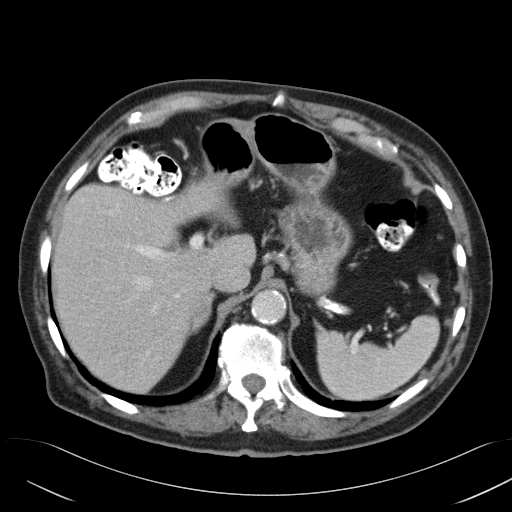
Contrast-enhanced abdominal CT, one axial slice; position 37 of 58 along the scan axis; reconstruction kernel B31f; intravenous contrast given; soft-tissue window (W 400 / L 40 HU); 5 mm slice thickness; 512 × 512 image matrix. Patient: male, 82 years. From the clinical record (not read from this slice): diagnosis: adrenocortical carcinoma; tumour side: right adrenal; tumour size at pathology: 9 cm; Ki-67 index: 30 %; stage (as recorded): 3.
Annotated regions visible in this slice (semi-automatic segmentation, software-assisted and operator-edited):
- mass: bounding box <193,298,212,326> (left, top, right, bottom; pixels)